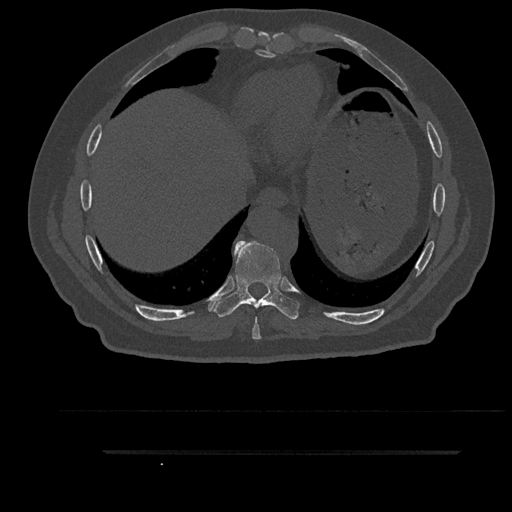
CT including the spine, one axial slice. Slice 436 of 797 in the series (ordered by position). 120 kVp. Bone window (W 1800 / L 400 HU). 0.5 mm slice thickness. 512 × 512 image matrix, field of view 432 × 432 mm. Male patient, age 63 years. From the clinical record (not read from this slice): primary cancer: renal; vertebrae with lytic lesions (as recorded): T8.
Outlined on this slice (semi-automatically segmented with operator editing):
- T8 vertebra: box from (x=252, y=305) to (x=272, y=340) px
- T9 vertebra: (x=212, y=241)–(x=299, y=320)